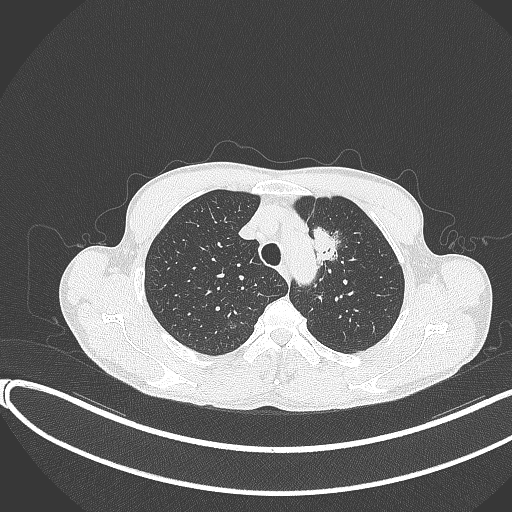
Chest CT, one axial slice. Slice 305 of 374 in the series (ordered by position). Lung window (W 1500 / L -600 HU). 1 mm slice thickness. 512 × 512 image matrix, field of view 400 × 400 mm. Male patient, age 58 years. From the clinical record (not read from this slice): clinical TNM (as recorded): T1c N1 M0.
Outlined on this slice (bounding box drawn by a radiologist):
- lung tumour (recorded histology: adenocarcinoma): bounding box (x1, y1, x2, y2) in pixels: (305, 222, 341, 268)